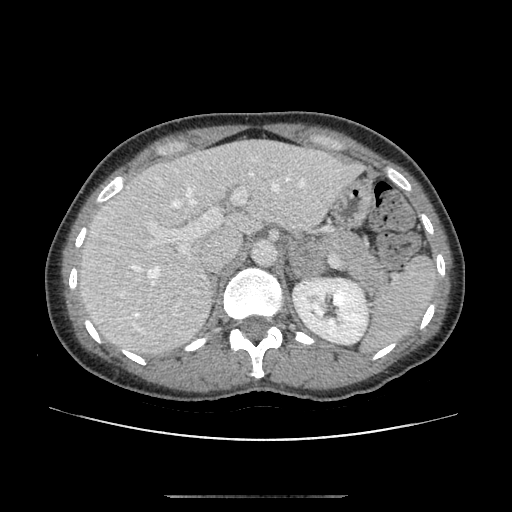
Contrast-enhanced abdominal CT, one axial slice; reconstruction kernel STANDARD; 120 kVp; soft-tissue window (W 400 / L 40 HU); 2.5 mm slice thickness; 512 × 512 image matrix. Patient: female, 51 years. From the clinical record (not read from this slice): diagnosis: adrenocortical carcinoma; tumour side: left adrenal; tumour size at pathology: 3.5 cm; Ki-67 index: 45 %; stage (as recorded): 1.
Outlined on this slice (semi-automatic segmentation, software-assisted and operator-edited):
- mass: bounding box <292,244,325,276> (left, top, right, bottom; pixels)